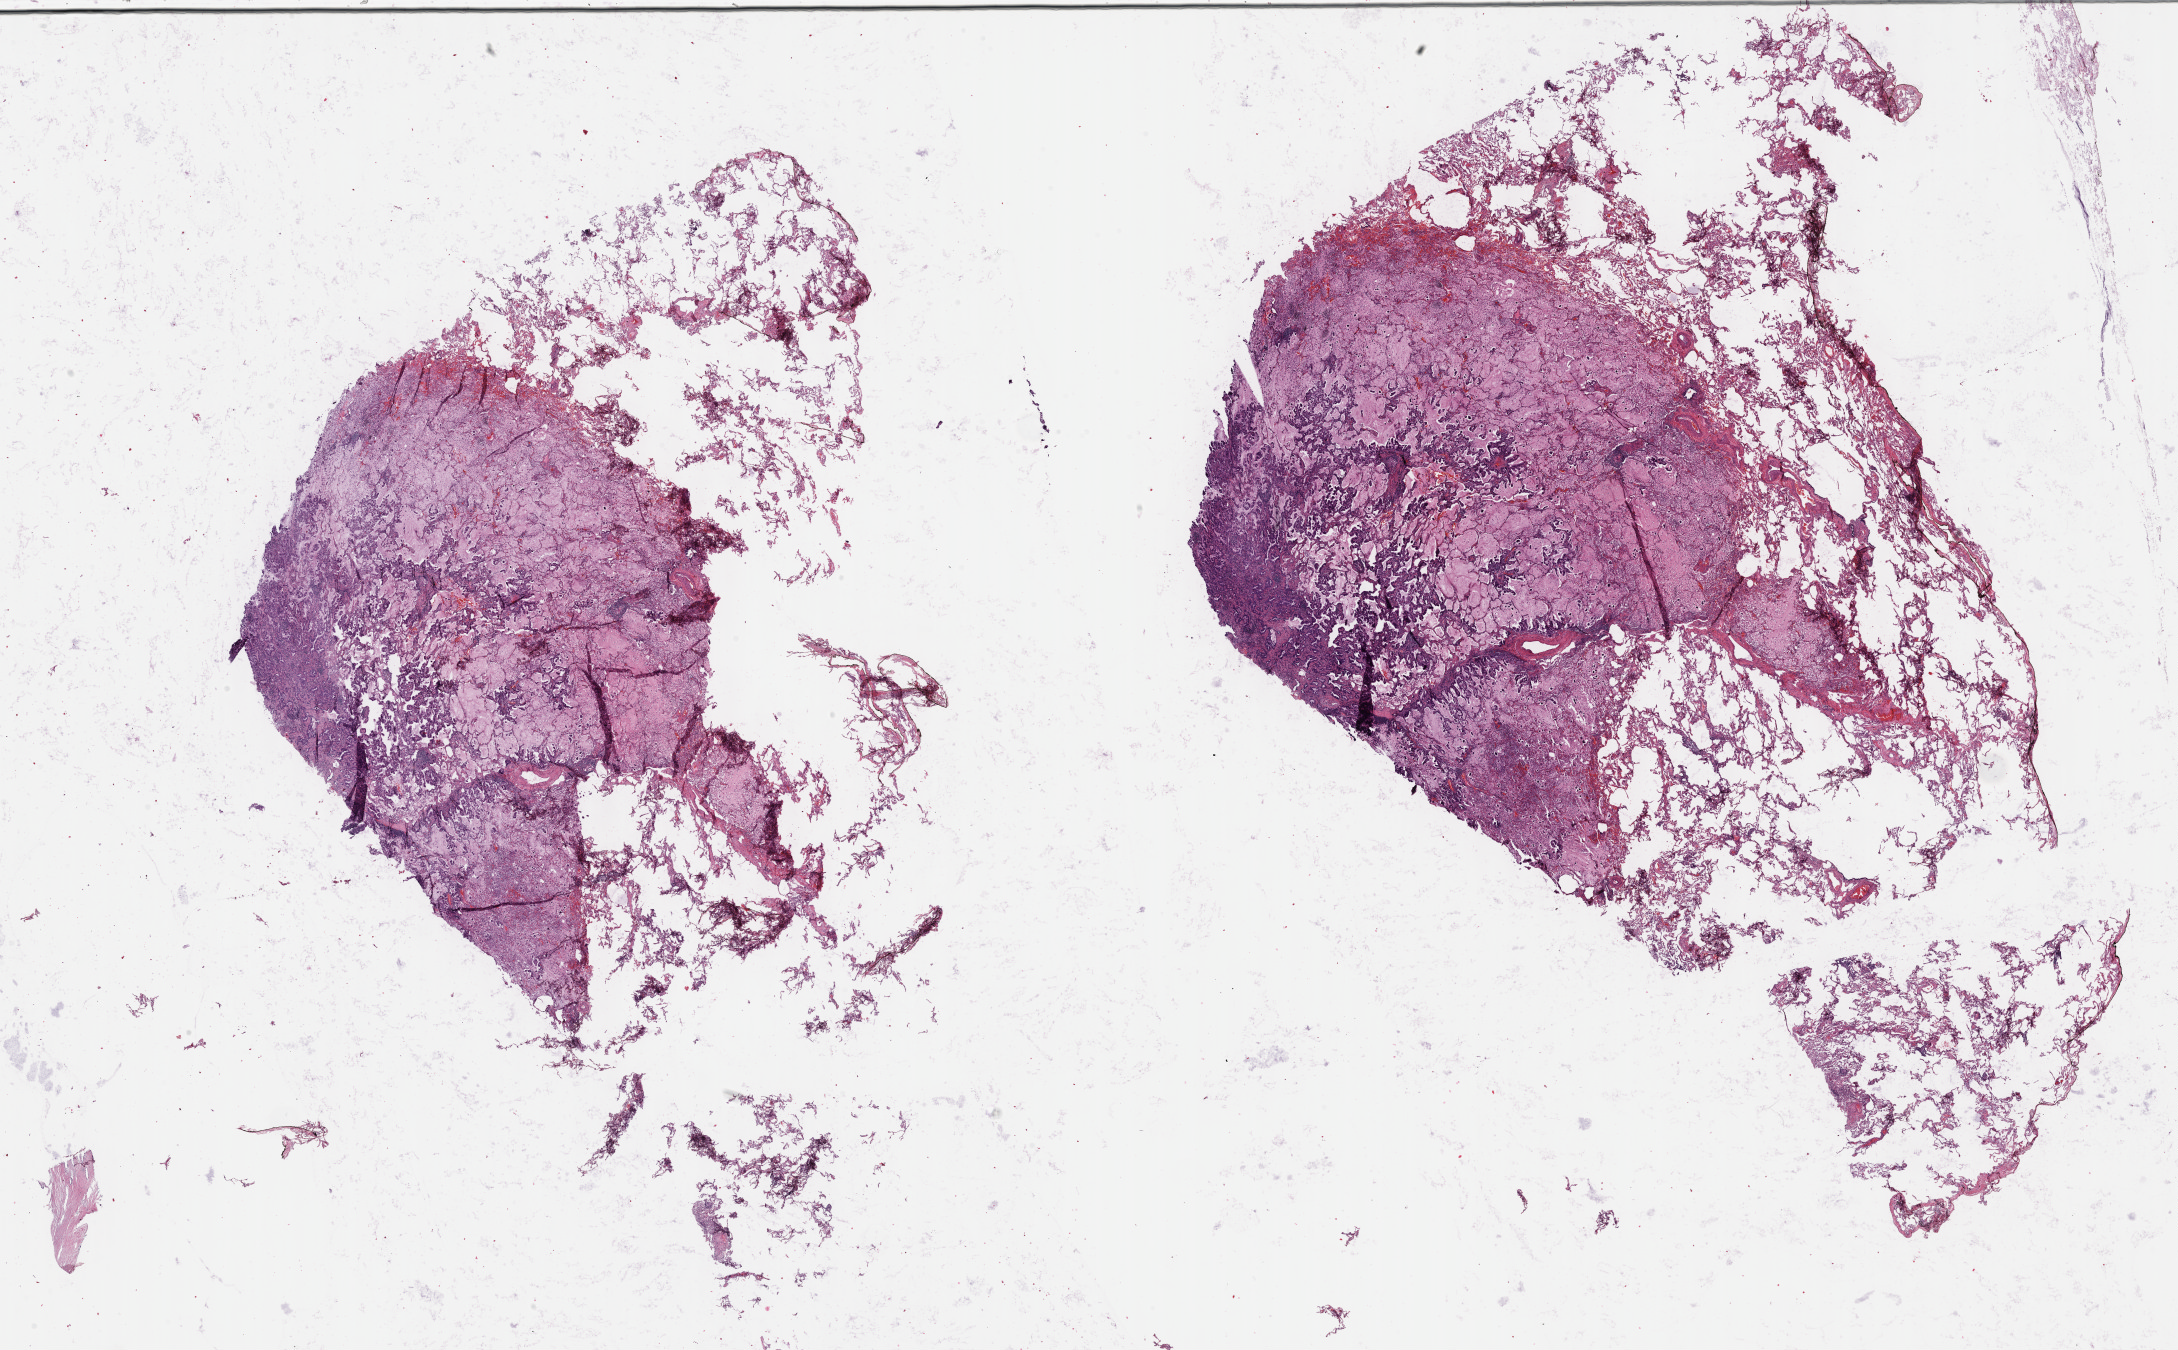
H&E-stained whole-slide image — a low-resolution overview of the entire scanned area, about 35.2 x 21.8 mm, FFPE section, lung, primary tumour sample. Female, age 56 years at initial diagnosis.
AJCC pathologic stage: IIA. Laterality: right. Diagnosis: Mucinous adenocarcinoma (upper lobe, lung).